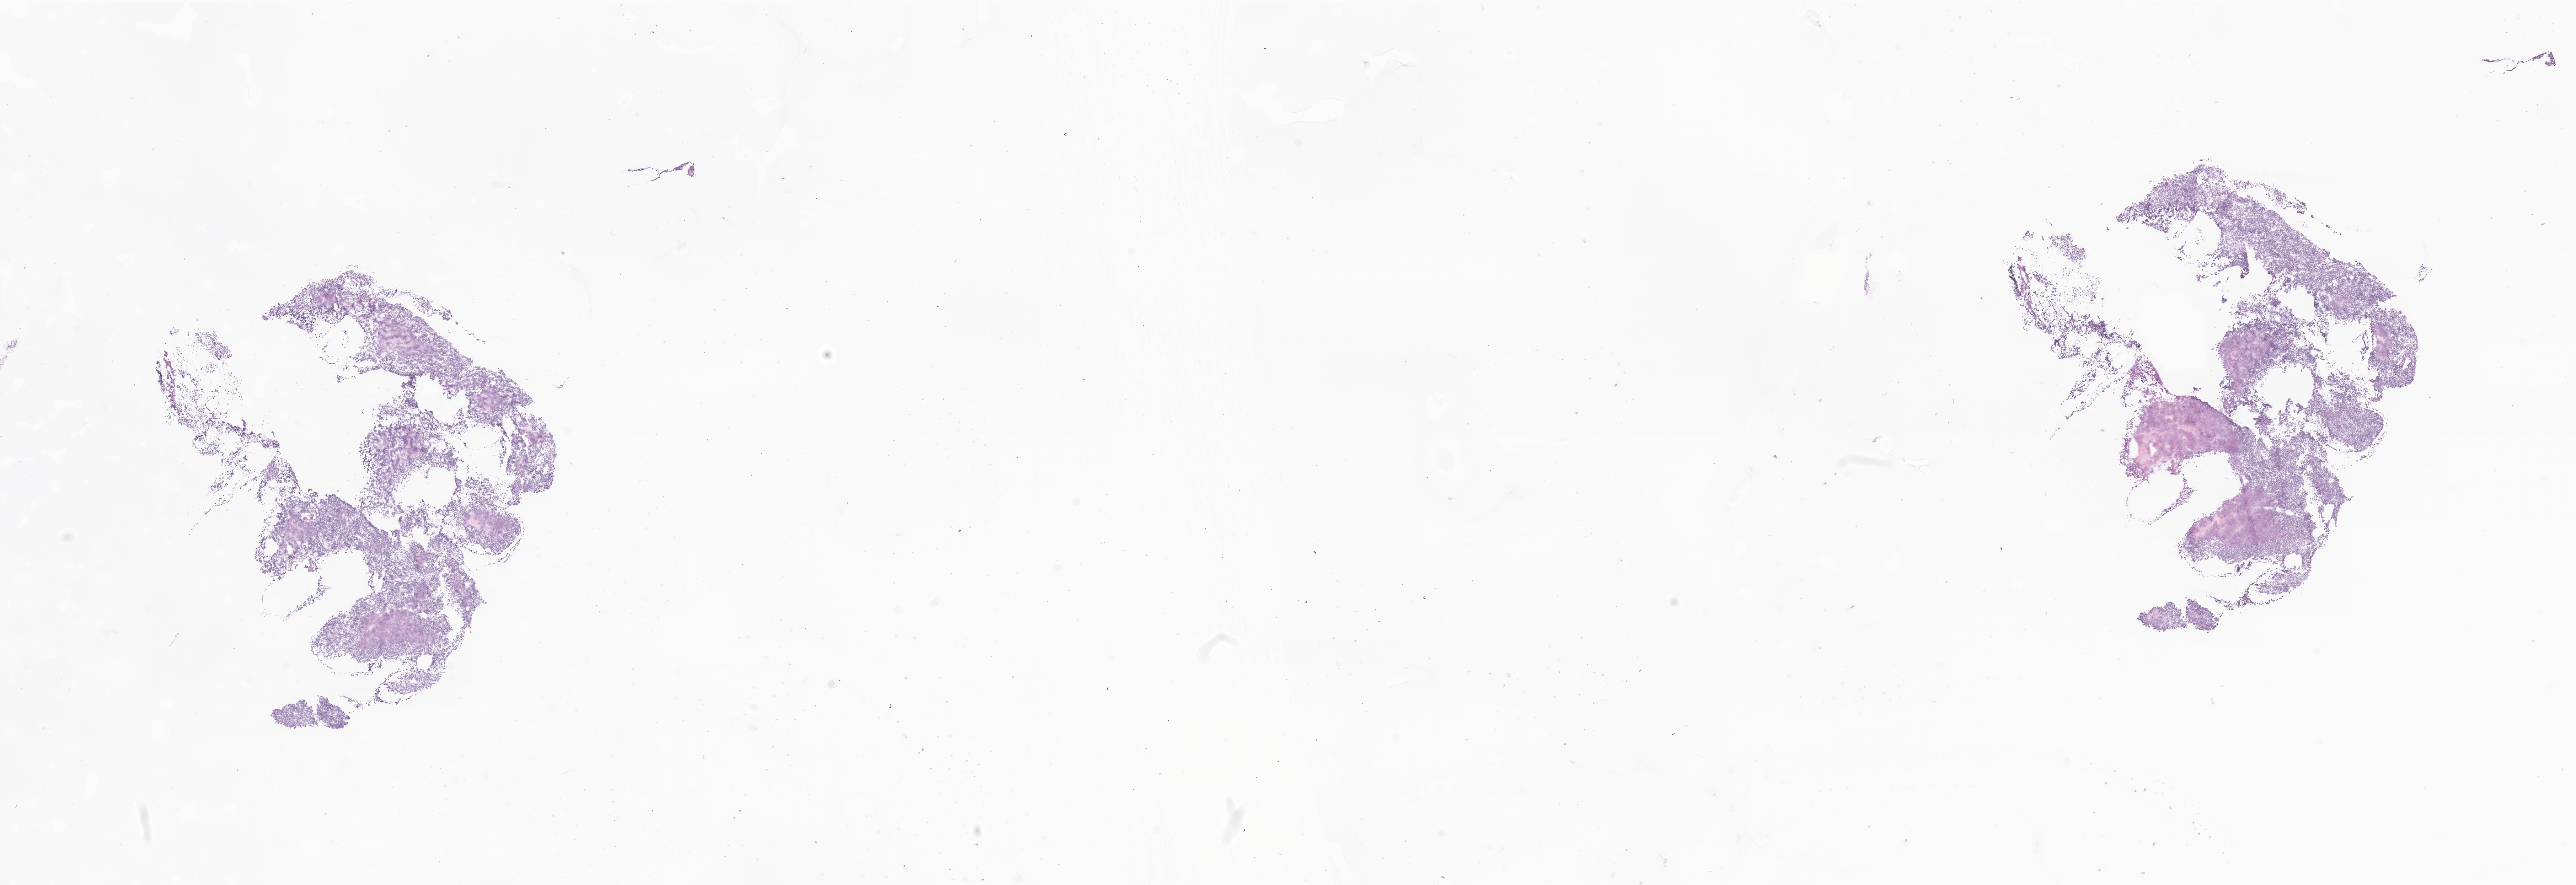
Digitized hematoxylin and eosin (H&E)-stained section of tumor tissue from the cerebellum, whole scanned area (about 30.6 x 10.5 mm) shown as a low-resolution overview; frozen section. Patient: male, age 102 months (8 years 6 months).
Recorded diagnosis: Medulloblastoma, NOS.